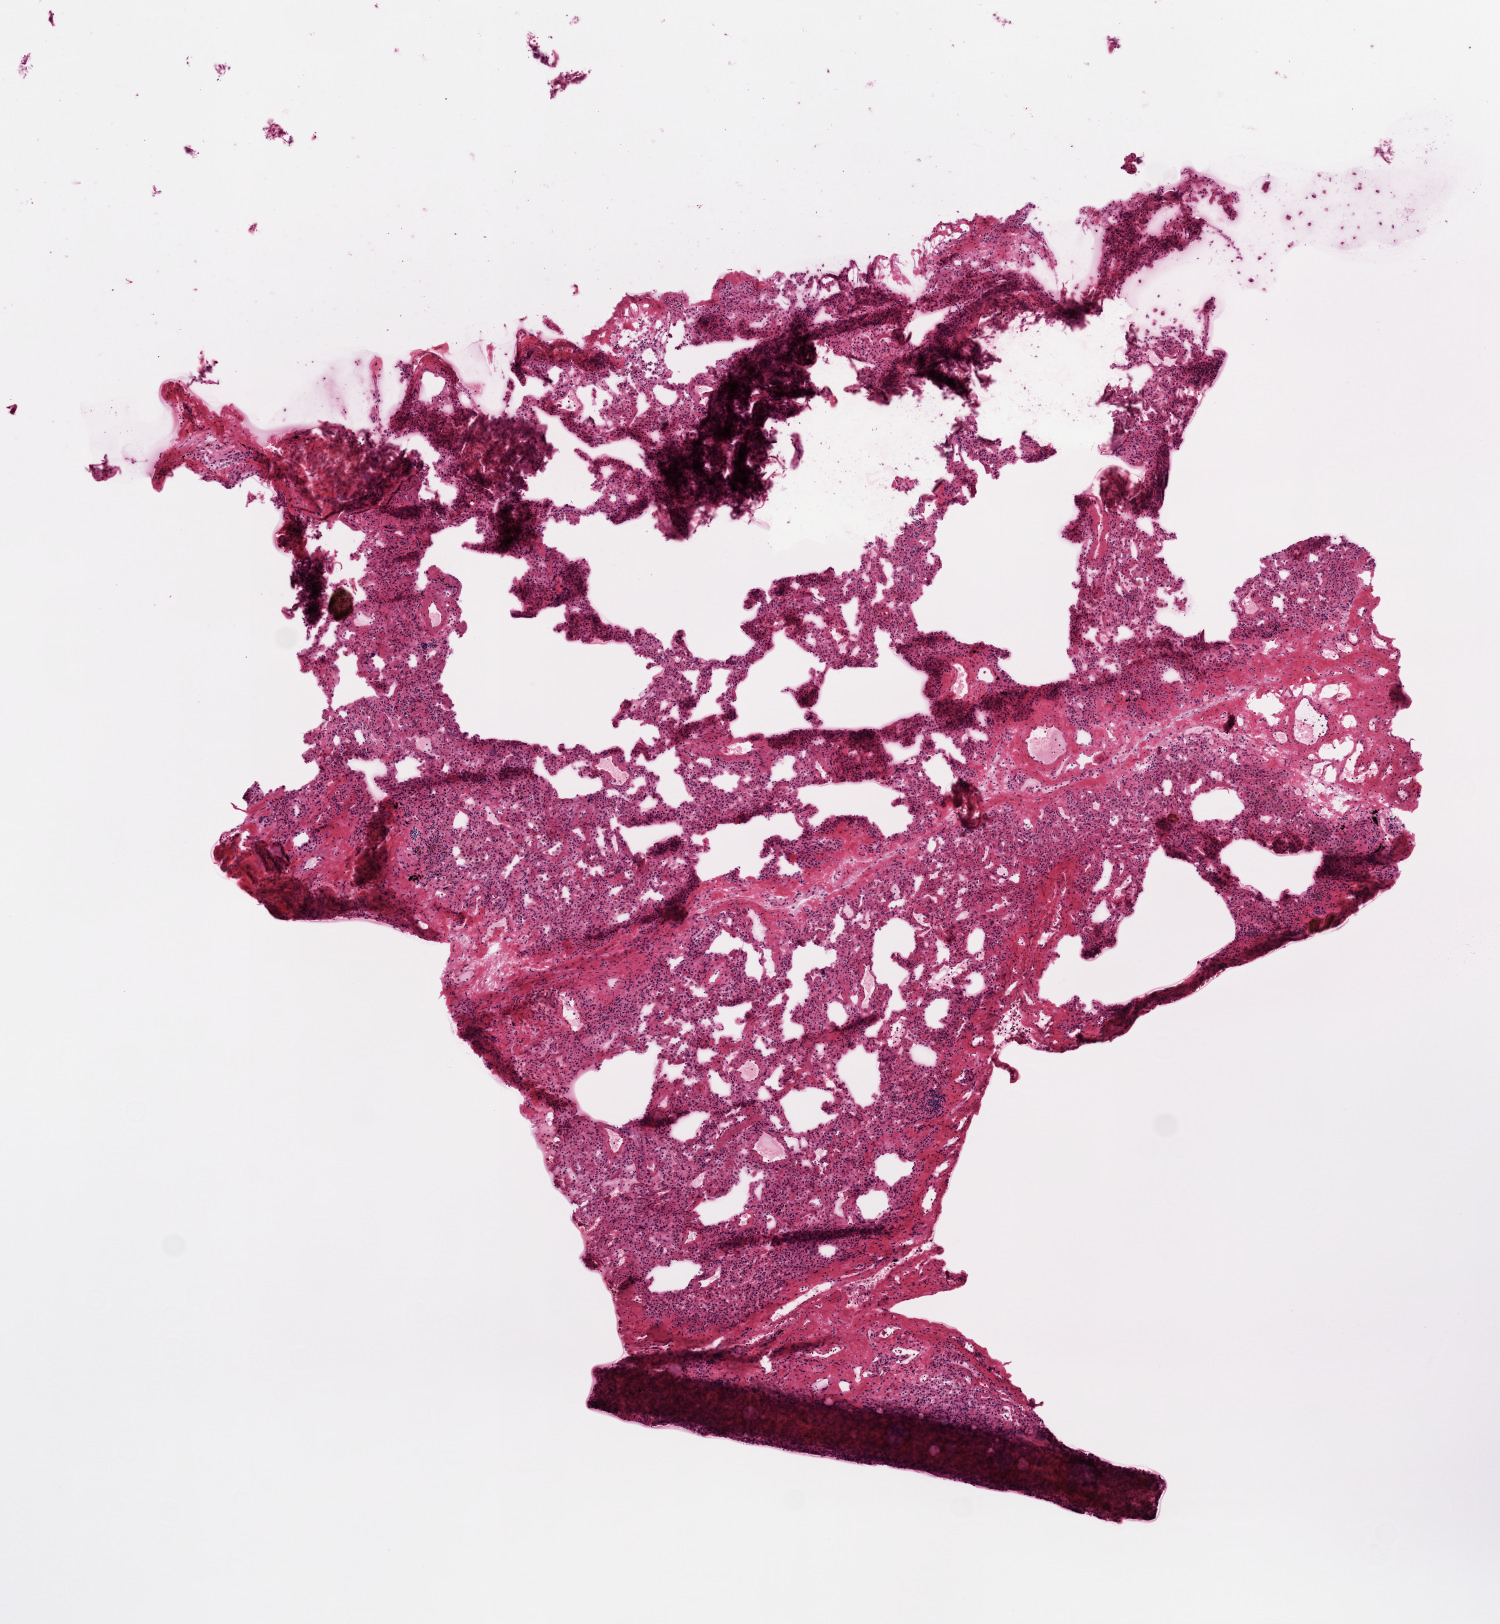
Digitized H&E-stained tissue section (whole slide), shown as a low-resolution overview of the whole scanned area (about 6.0 x 6.5 mm, acquisition: 20x scan); frozen section from the top of the tissue portion; solid tissue normal (non-tumour tissue) sample from the lung. Male, age 66 years at initial diagnosis.
This section: solid tissue normal sample (biorepository sample class). Patient diagnosis: Squamous cell carcinoma, NOS (upper lobe, lung).